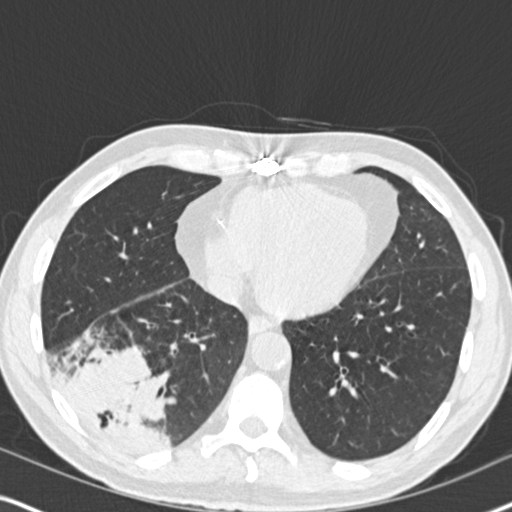
Axial slice from a low-dose chest CT screening exam. Second annual screen. Lung window (W 1500 / L -600 HU). Male participant, aged 61 years at enrolment.
Expert reader's lesion annotation, box from (x=43, y=316) to (x=187, y=462) px. The exam's reader record, not a measurement of the box and not confirmed to be the same lesion: non-calcified nodule or mass ≥4 mm, right lower lobe, 90 × 80 mm, soft tissue attenuation, pre-existing on the prior screen: yes; interval growth: yes. Official screen result: positive, other. Lung cancer was diagnosed 20 days after this screen: bronchiolo-alveolar adenocarcinoma, NOS, right lower lobe, moderately differentiated (G2), stage IIIB (AJCC 6th edition), 90 mm at pathology.